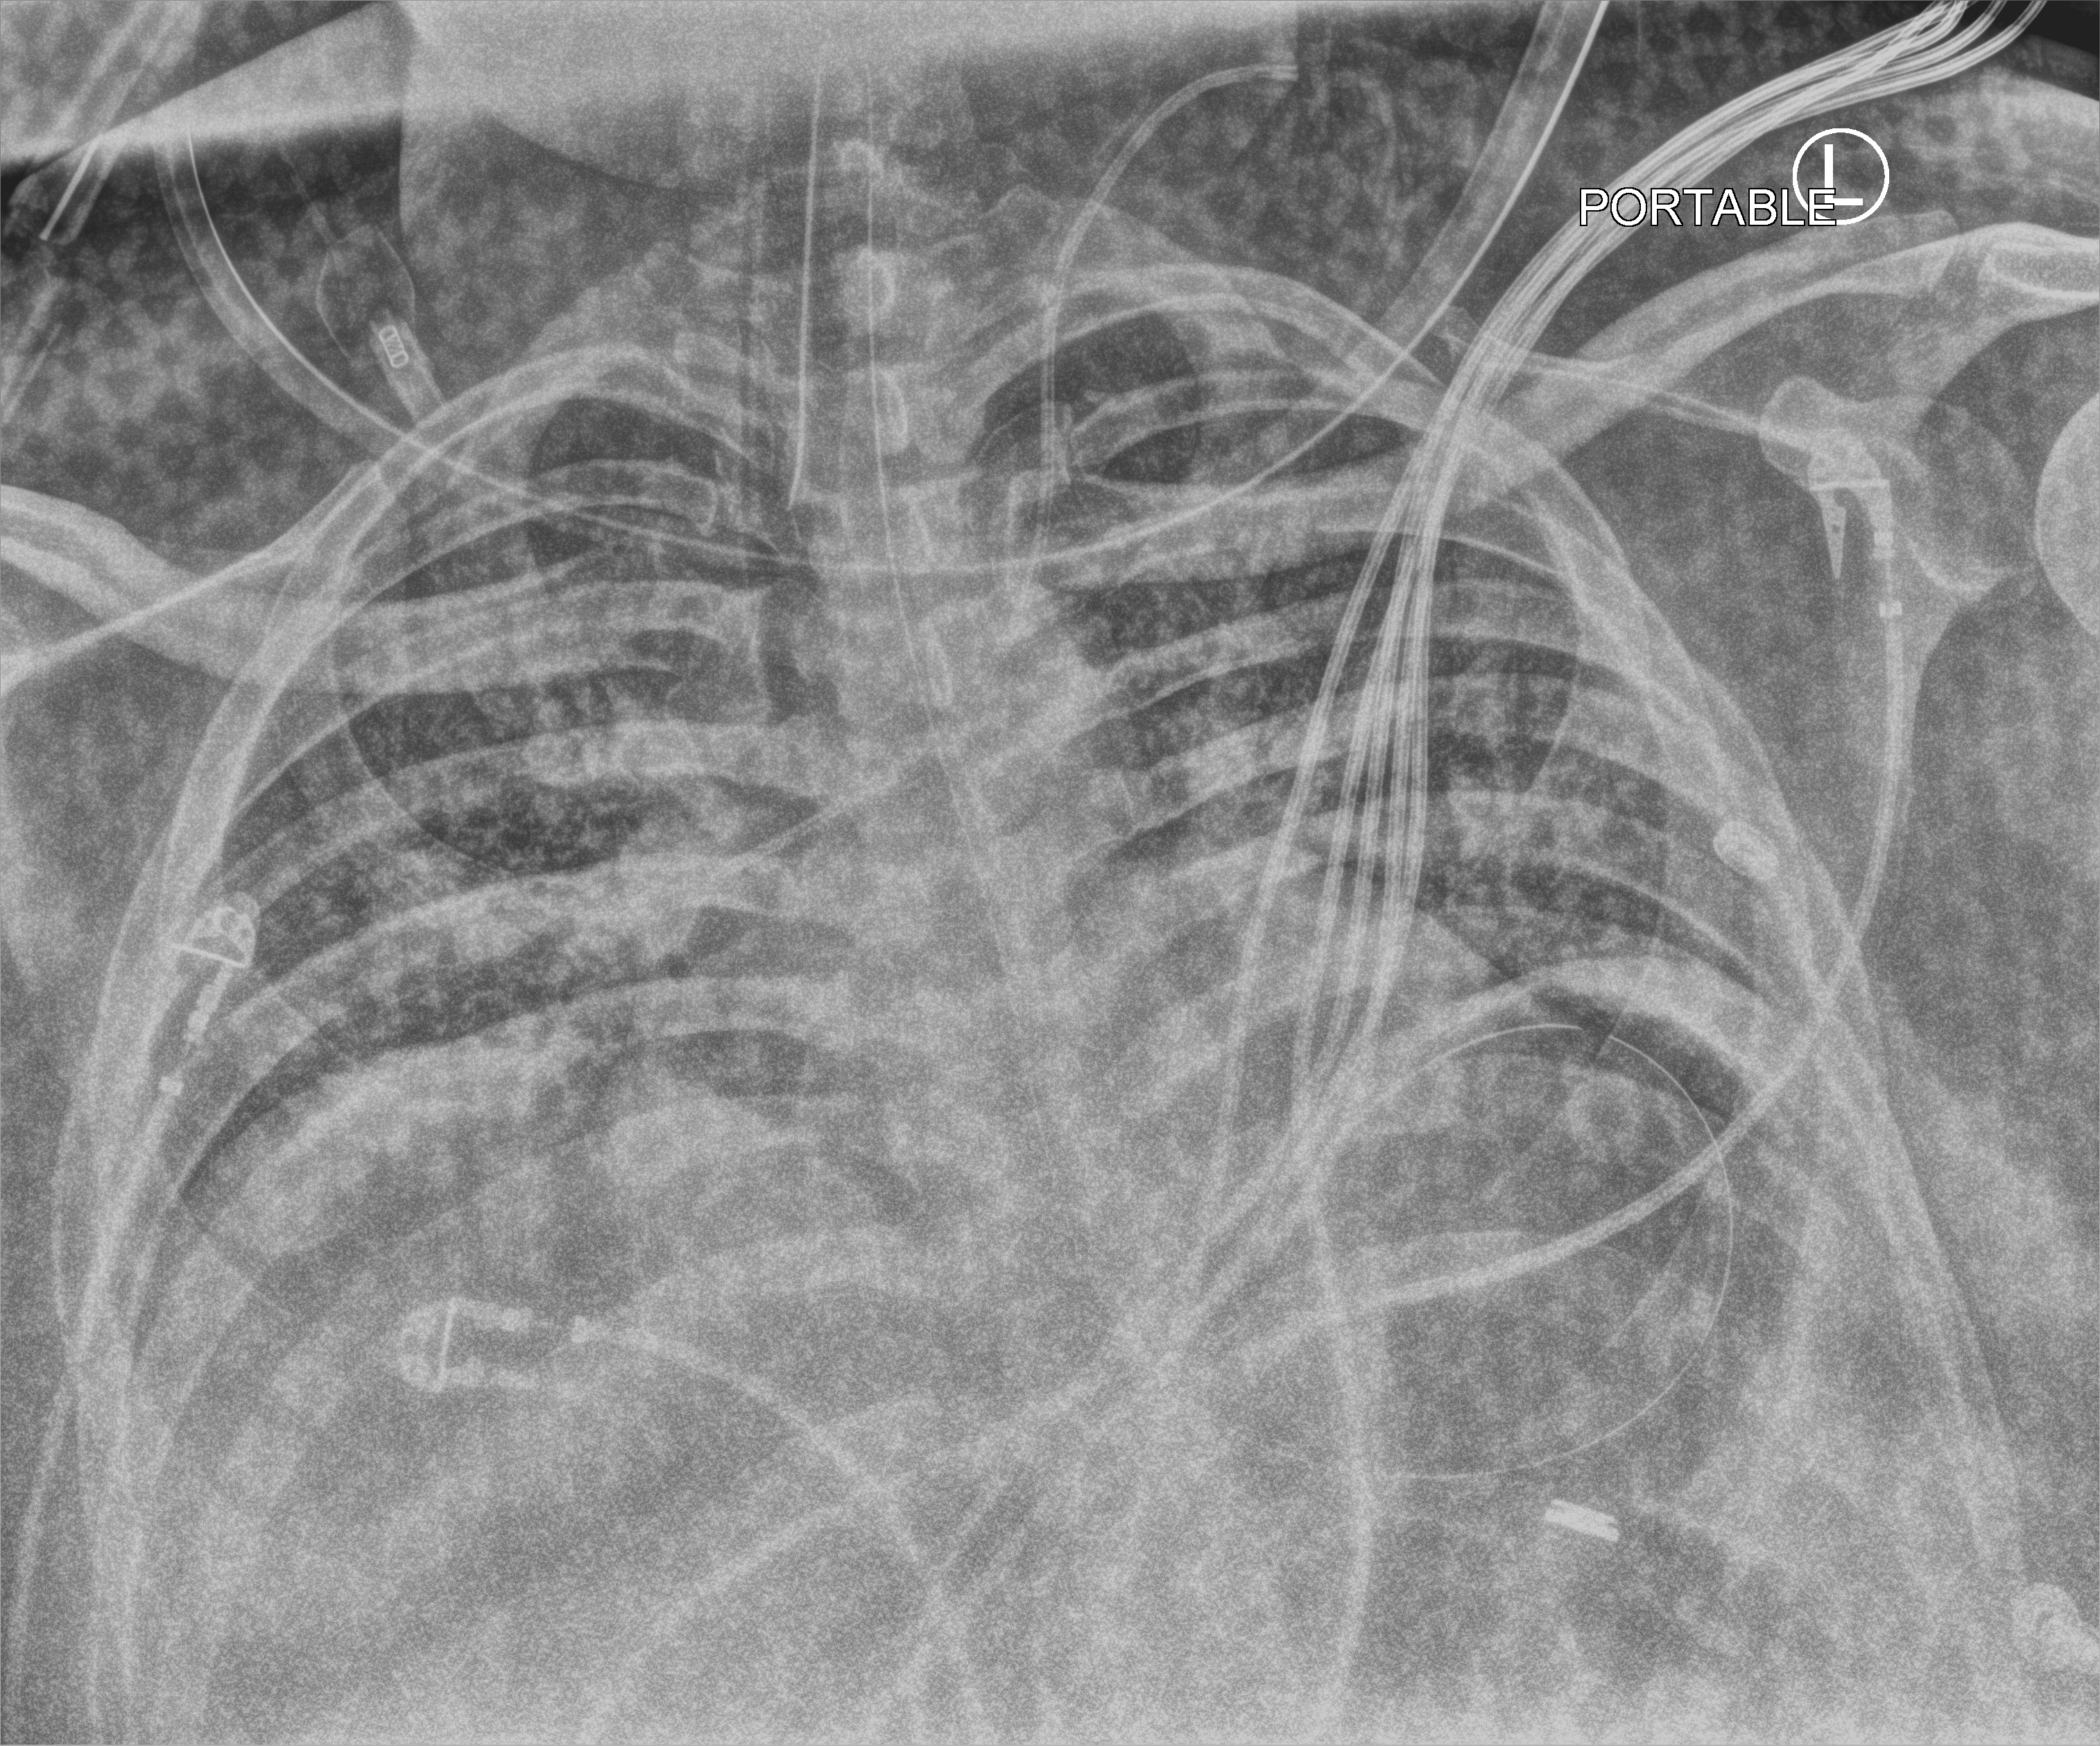
Portable chest radiograph. Male patient hospitalised with COVID-19, age 18–59 years.
Admission-level facts for this patient (not findings on this image; timing relative to this image not recorded): mechanically ventilated during this hospital stay: yes; admitted to intensive care during this hospital stay: yes; hypertension (admission record): no.